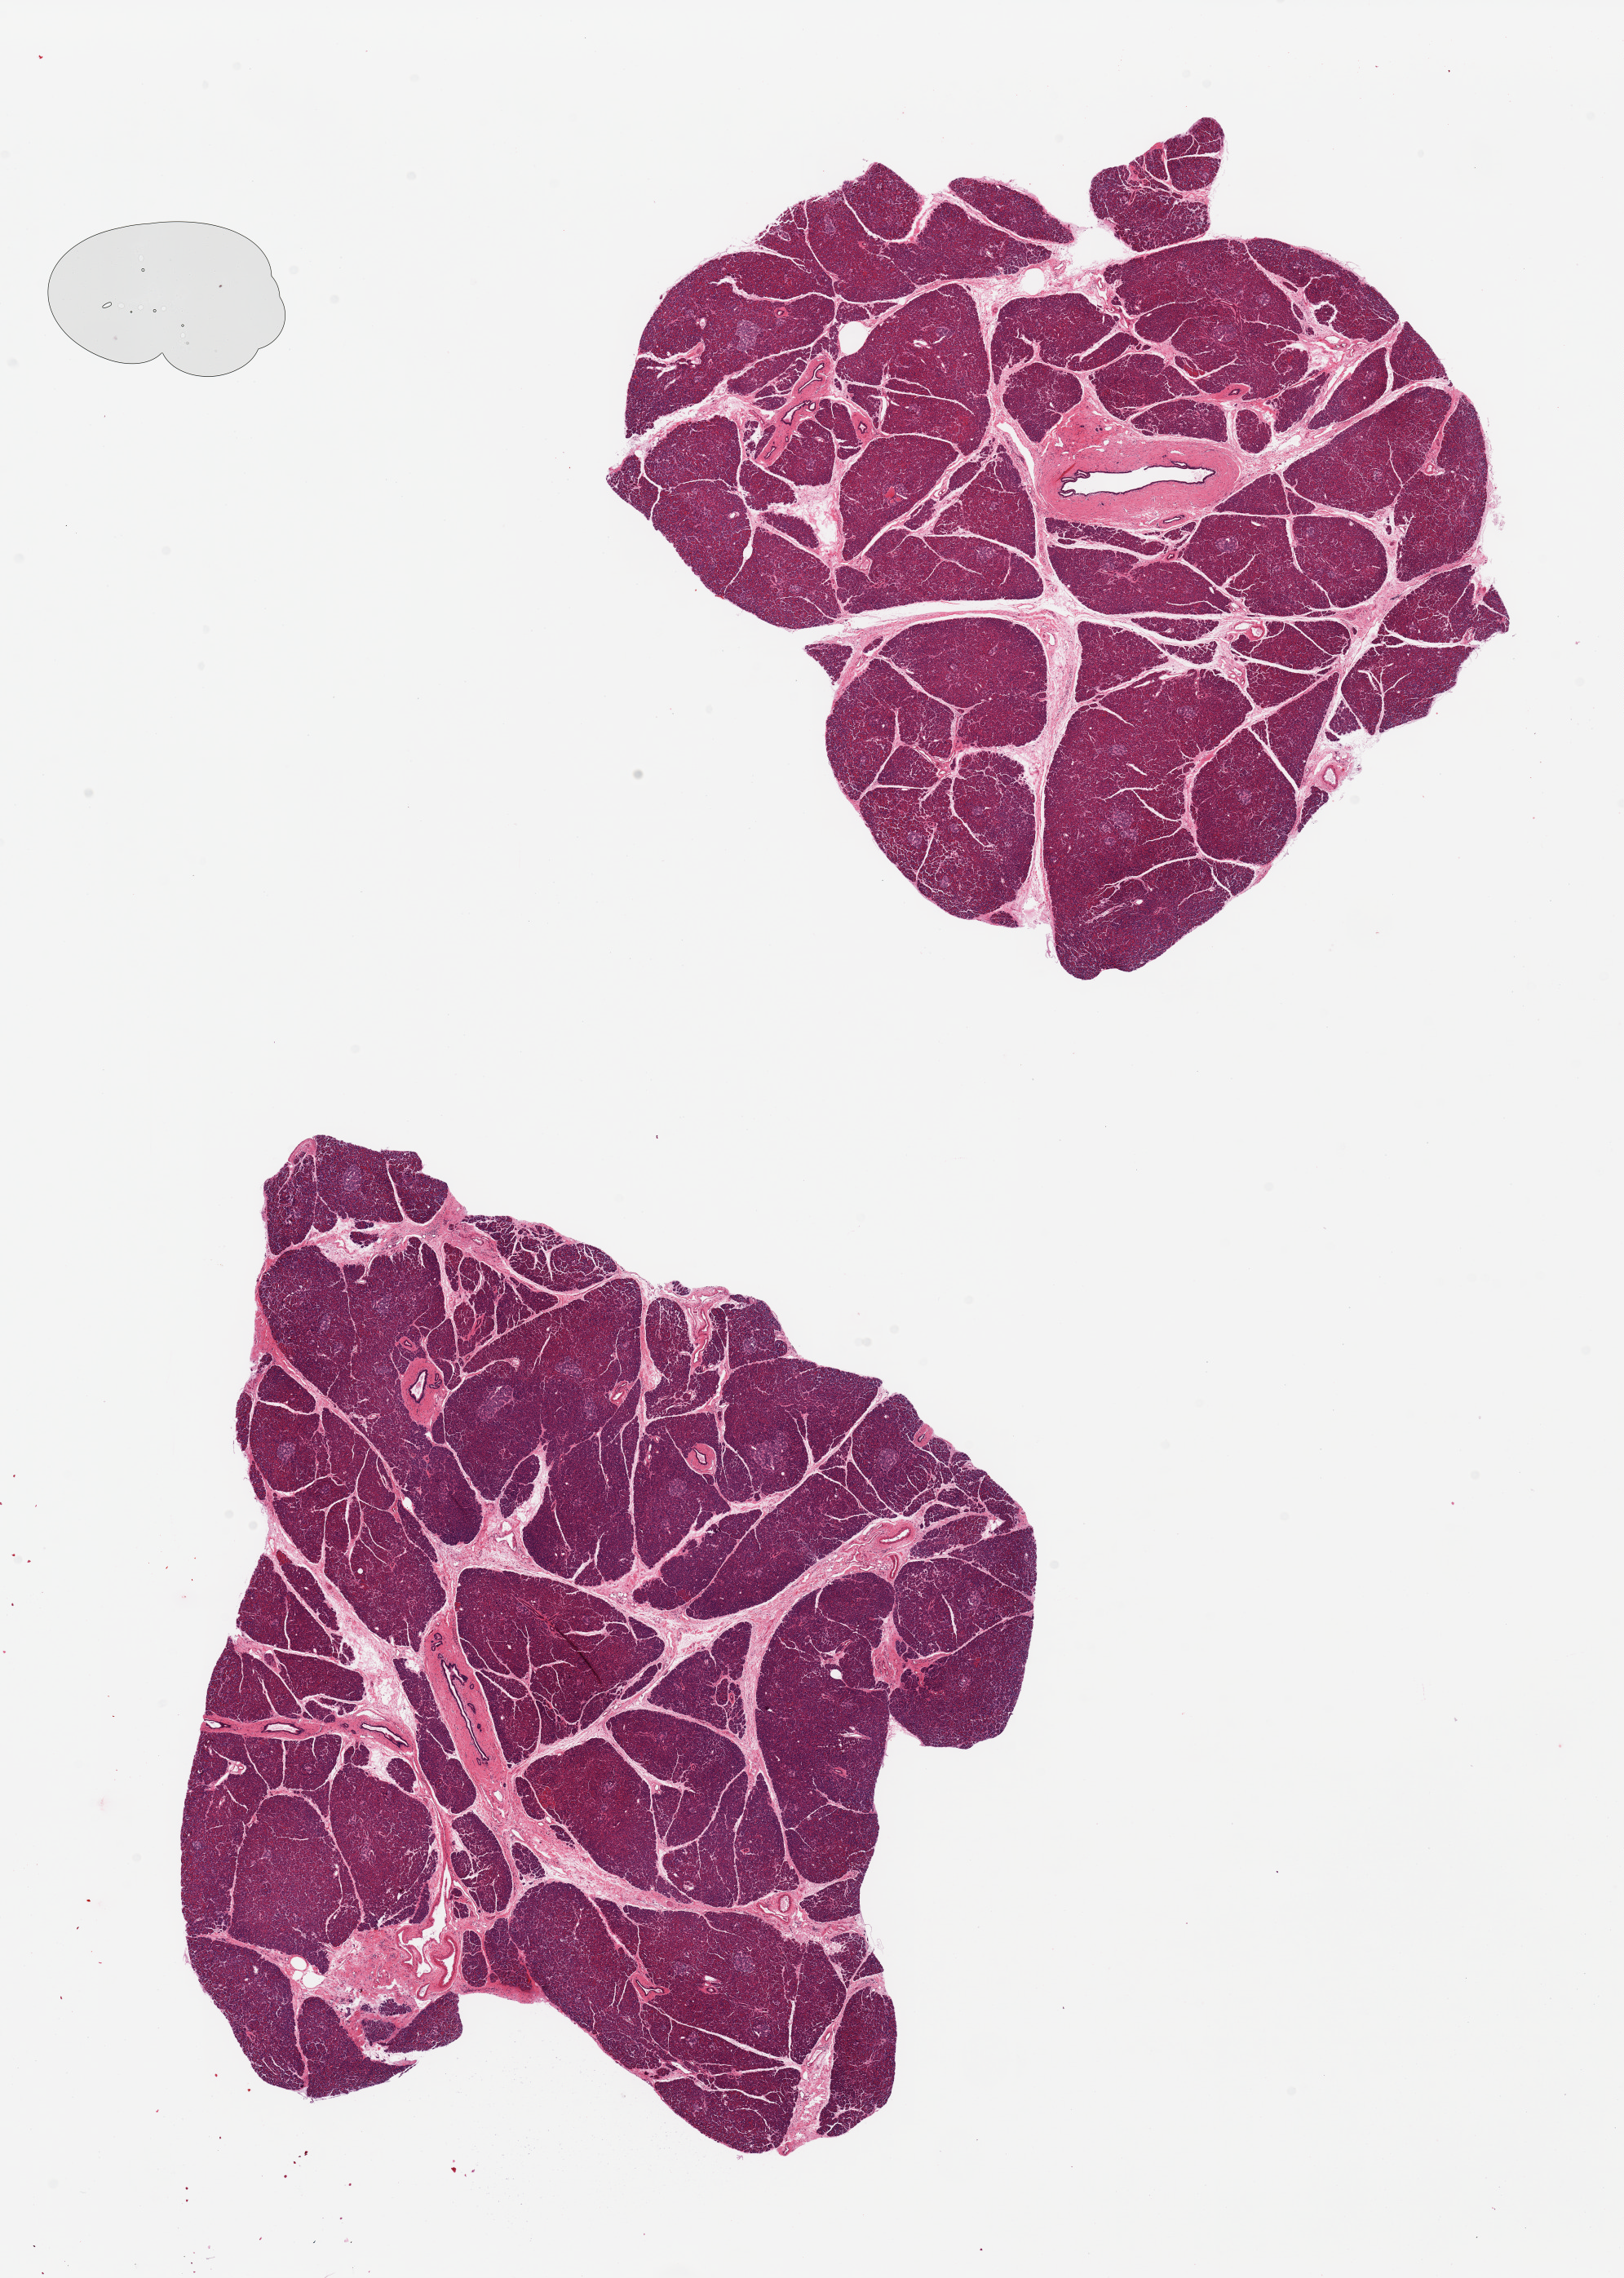
Whole-slide image, haematoxylin and eosin stain, a low-resolution overview of the entire scanned area, about 15.8 x 22.1 mm, PAXgene-fixed paraffin-embedded (PFPE) section, section of pancreas (target tissue), donor tissue sample. Male donor.
Reviewer comment on this tissue sample: 2 pieces; well trimmed.